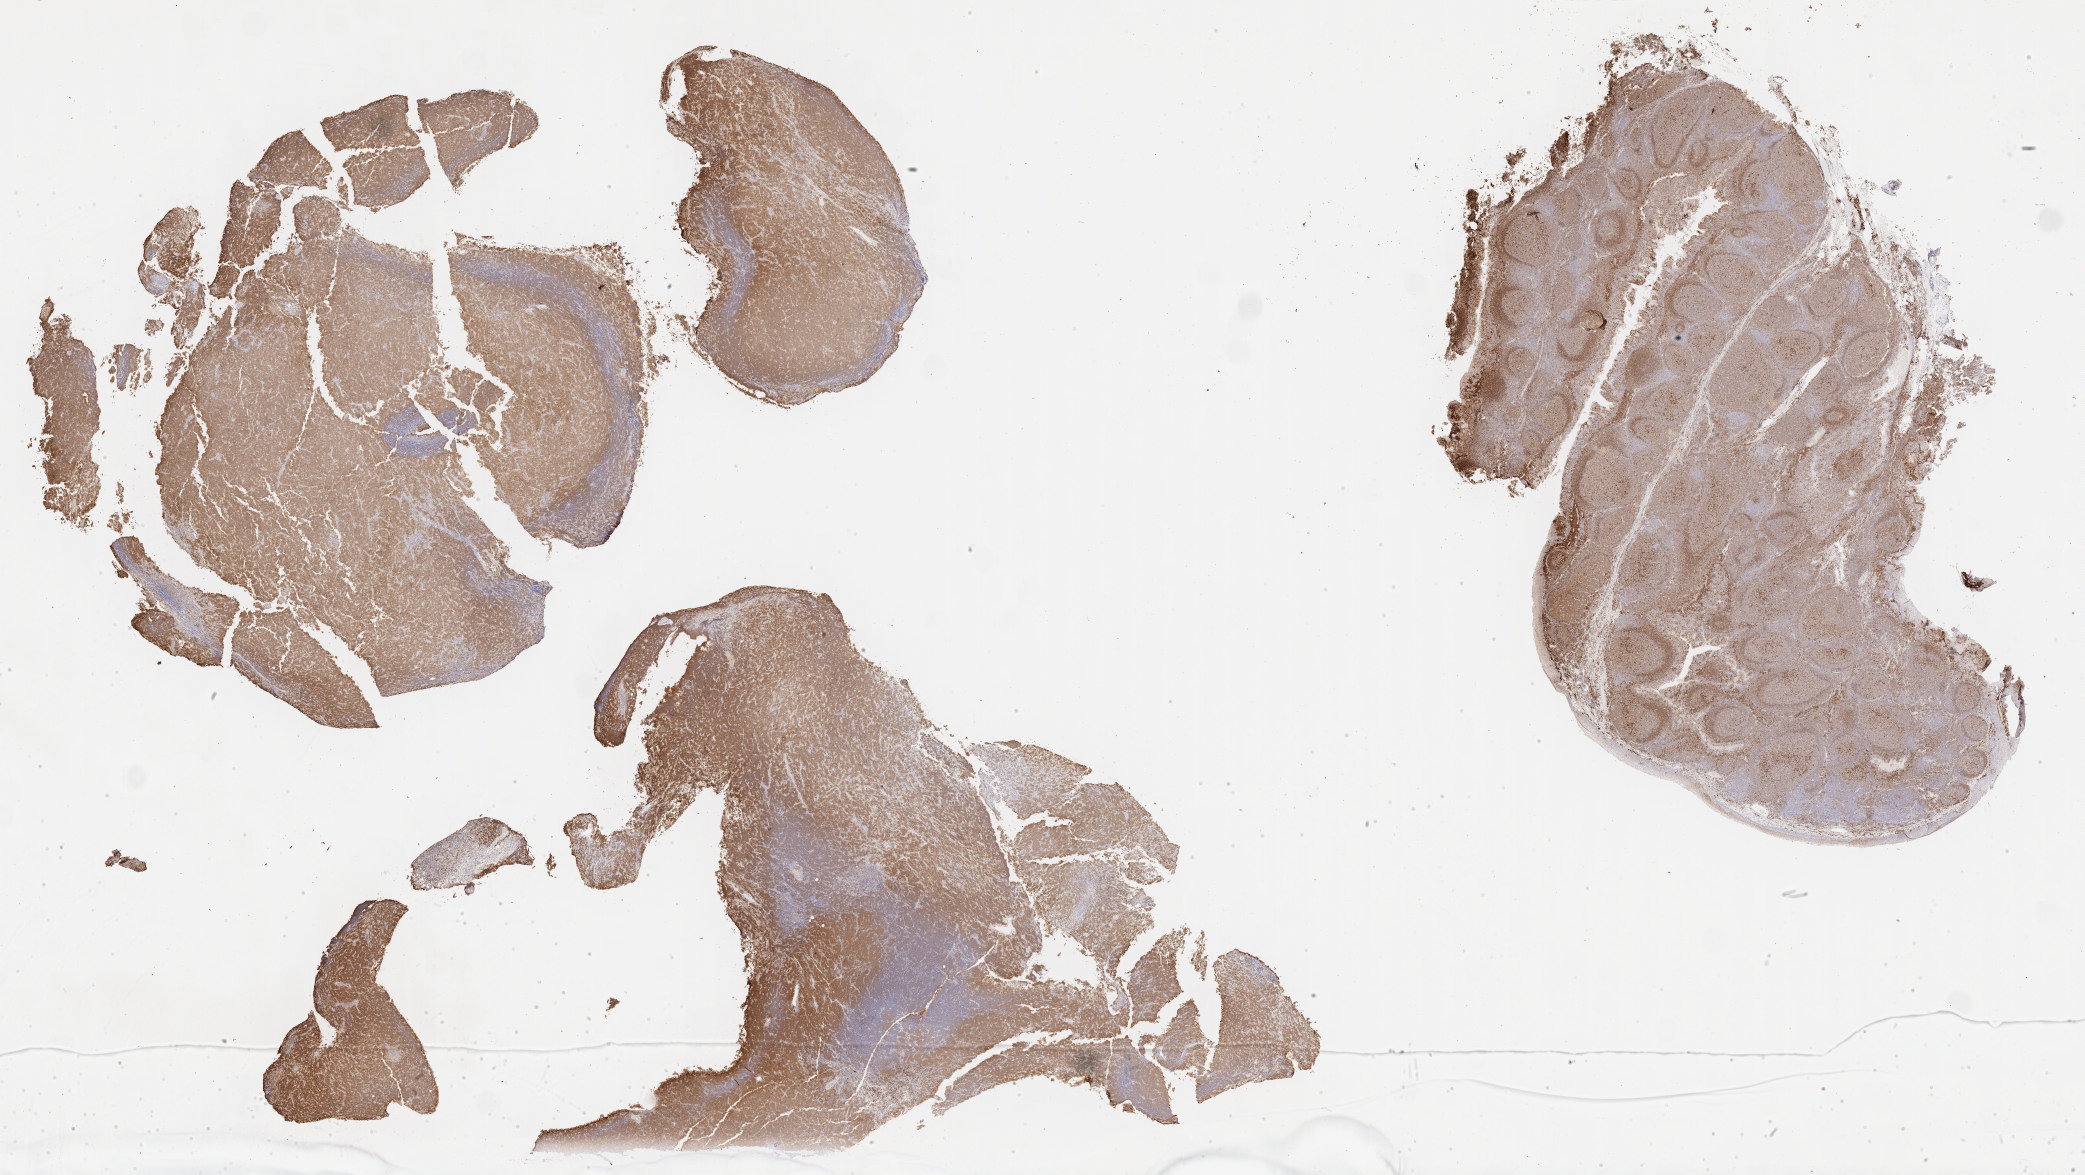
Whole-slide image, immunohistochemical stain for CD79a, shown as a low-resolution overview of the whole scanned area (about 33.7 x 19.0 mm); tumor tissue; anatomic site: liver. Patient: male, age 45 years.
Diagnosis: Diffuse large B-cell lymphoma, NOS.